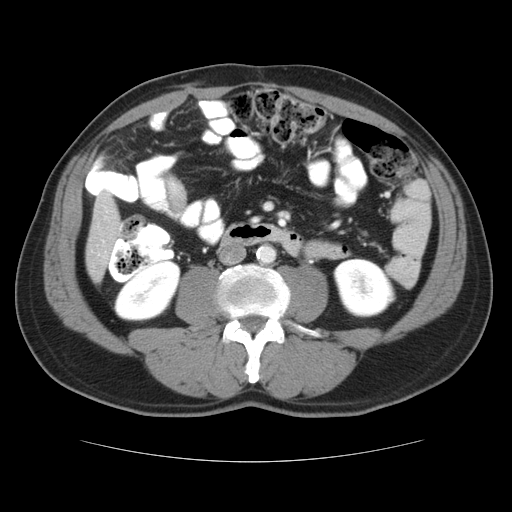
Contrast-enhanced abdominal CT, one axial slice; slice 7 of 37 in the series (ordered by position); reconstruction kernel STANDARD; 120 kVp; soft-tissue window (W 400 / L 40 HU); 512 × 512 image matrix, field of view 374 × 374 mm. Male patient, age 66 years. From the clinical record (not read from this slice): diagnosis: colorectal cancer liver metastases, imaged before liver resection; multiple liver metastases: yes; largest metastasis: 1.6 cm; disease in both lobes: yes.
Structures marked on this image (manually delineated by an expert):
- hepatic veins: bounding box (x1, y1, x2, y2) in pixels: (98, 206, 111, 257)
- liver: (86, 190, 122, 281)
- planned liver remnant (the part of the liver to remain after resection): (86, 190, 122, 281)